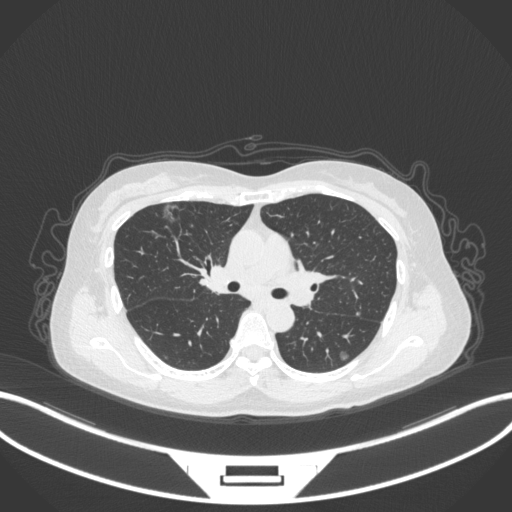
Chest CT, one axial slice. Slice 201 of 317 in the series (ordered by position). Reconstruction kernel B31f. Lung window (W 1500 / L -600 HU). 512 × 512 image matrix, field of view 400 × 400 mm. Patient: female, 61 years. From the clinical record (not read from this slice): clinical TNM (as recorded): T1b N0 M0.
Outlined on this slice (bounding box drawn by a radiologist):
- lung tumour (recorded histology: adenocarcinoma): box from (x=159, y=199) to (x=185, y=225) px